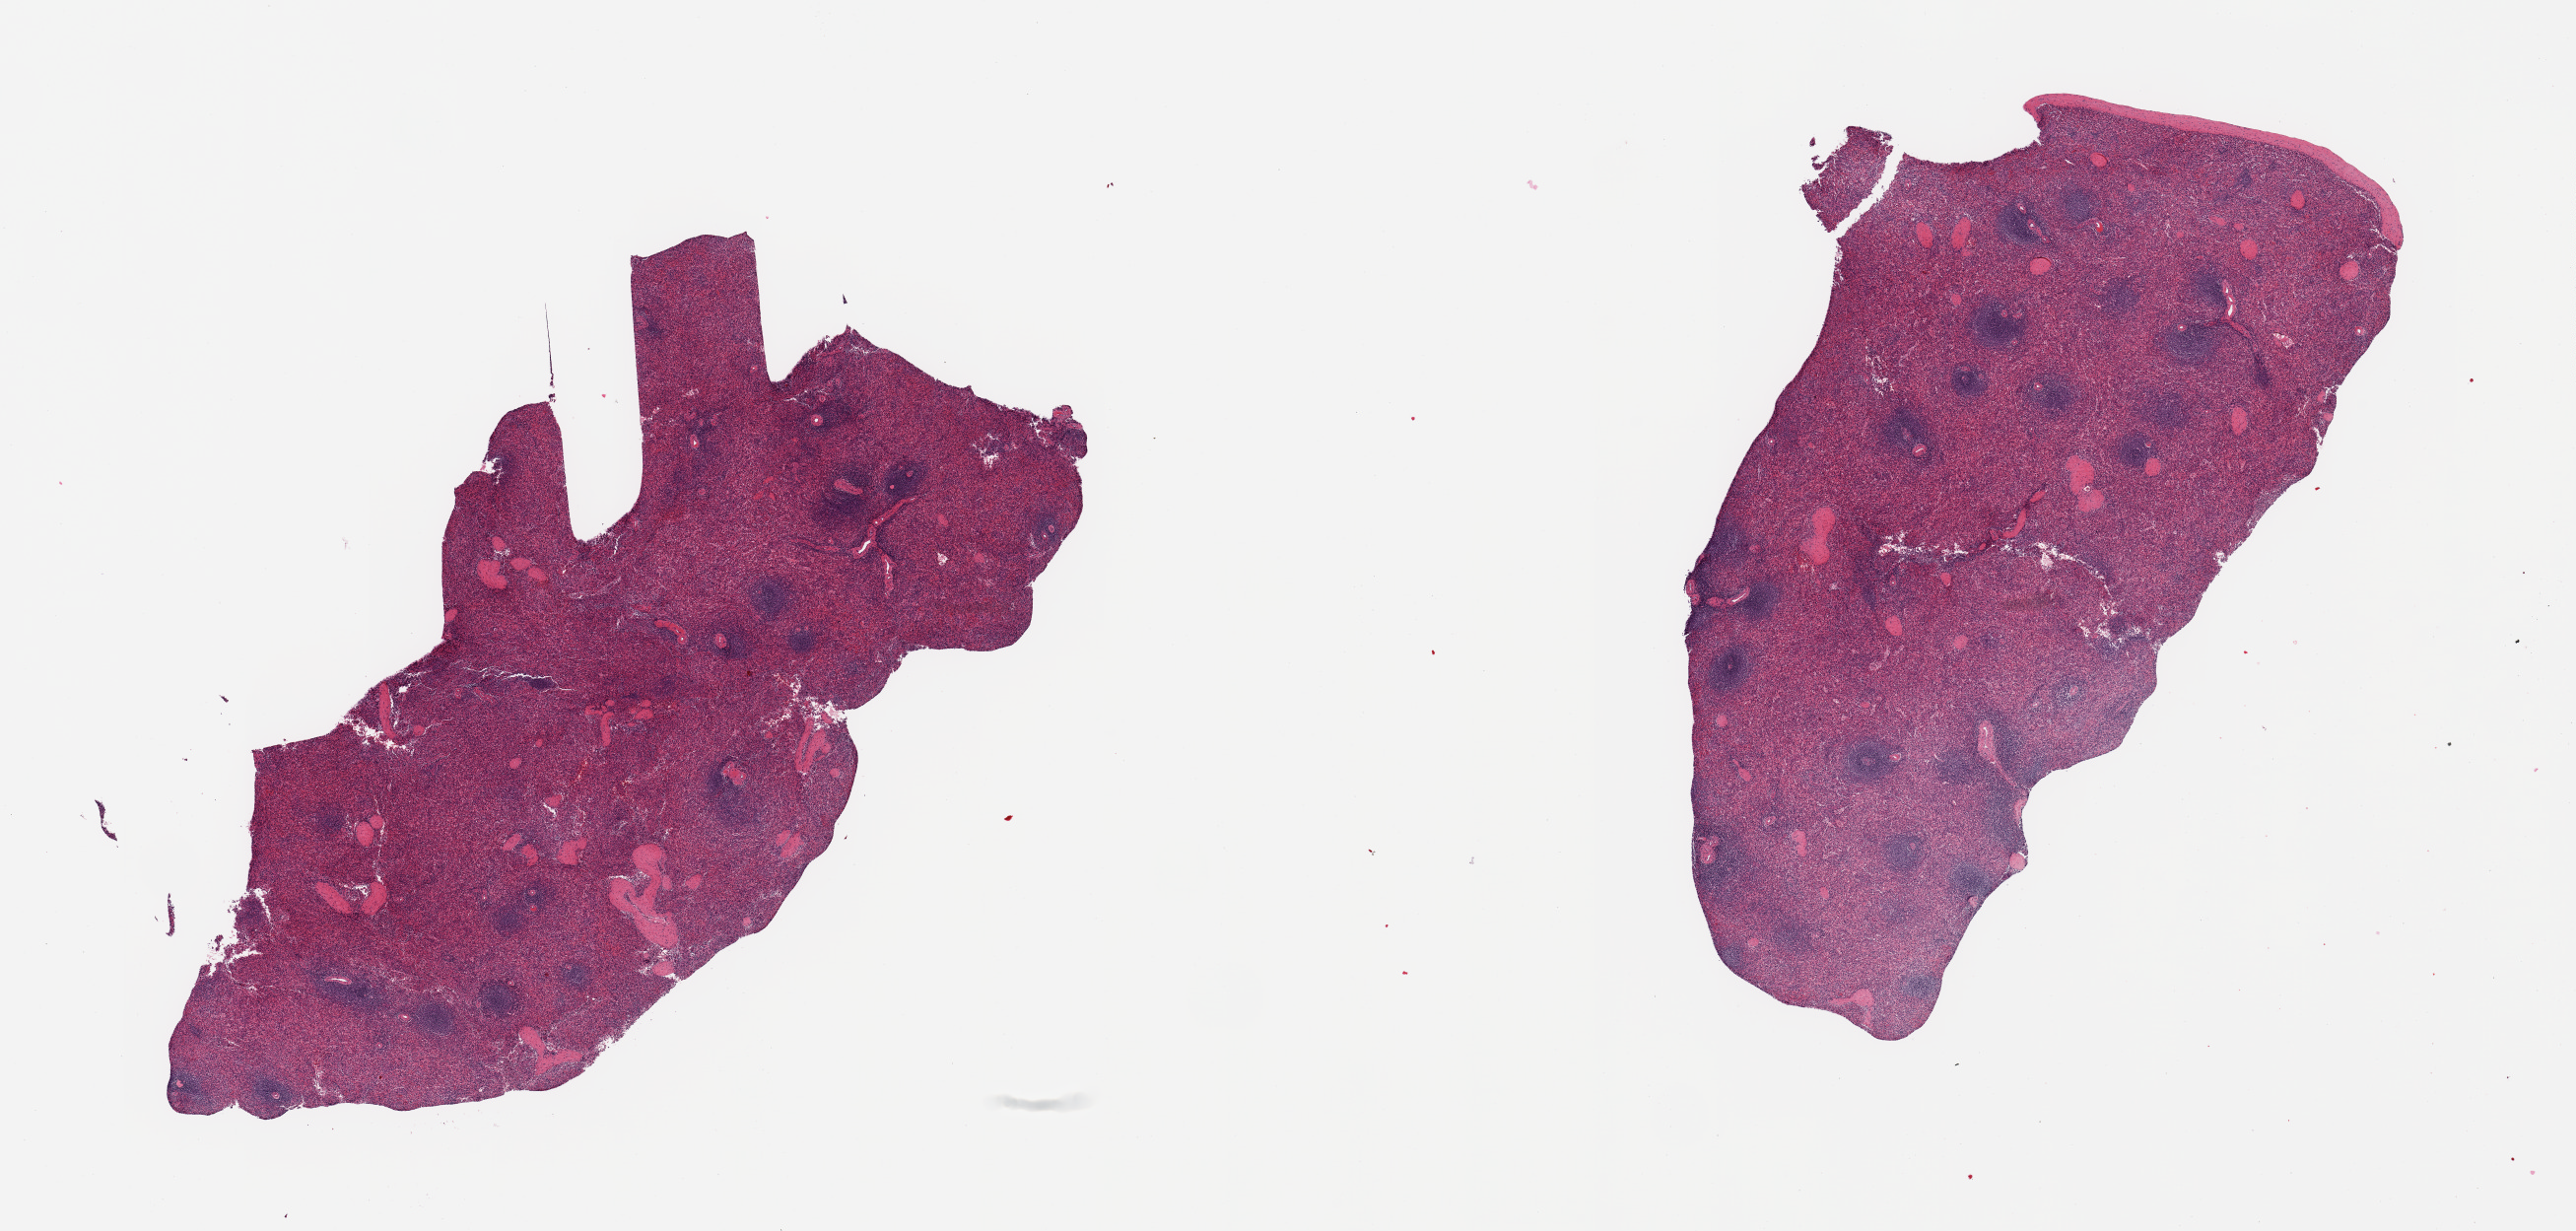
Haematoxylin and eosin whole-slide image, brightfield, a low-resolution overview of the entire scanned area, about 20.7 x 9.9 mm (from a 20x scan). PAXgene-fixed paraffin-embedded (PFPE) section. Target tissue: spleen. Tissue donor sample. Donor: male.
Review note (as recorded): 2 pieces, no abnormalities.